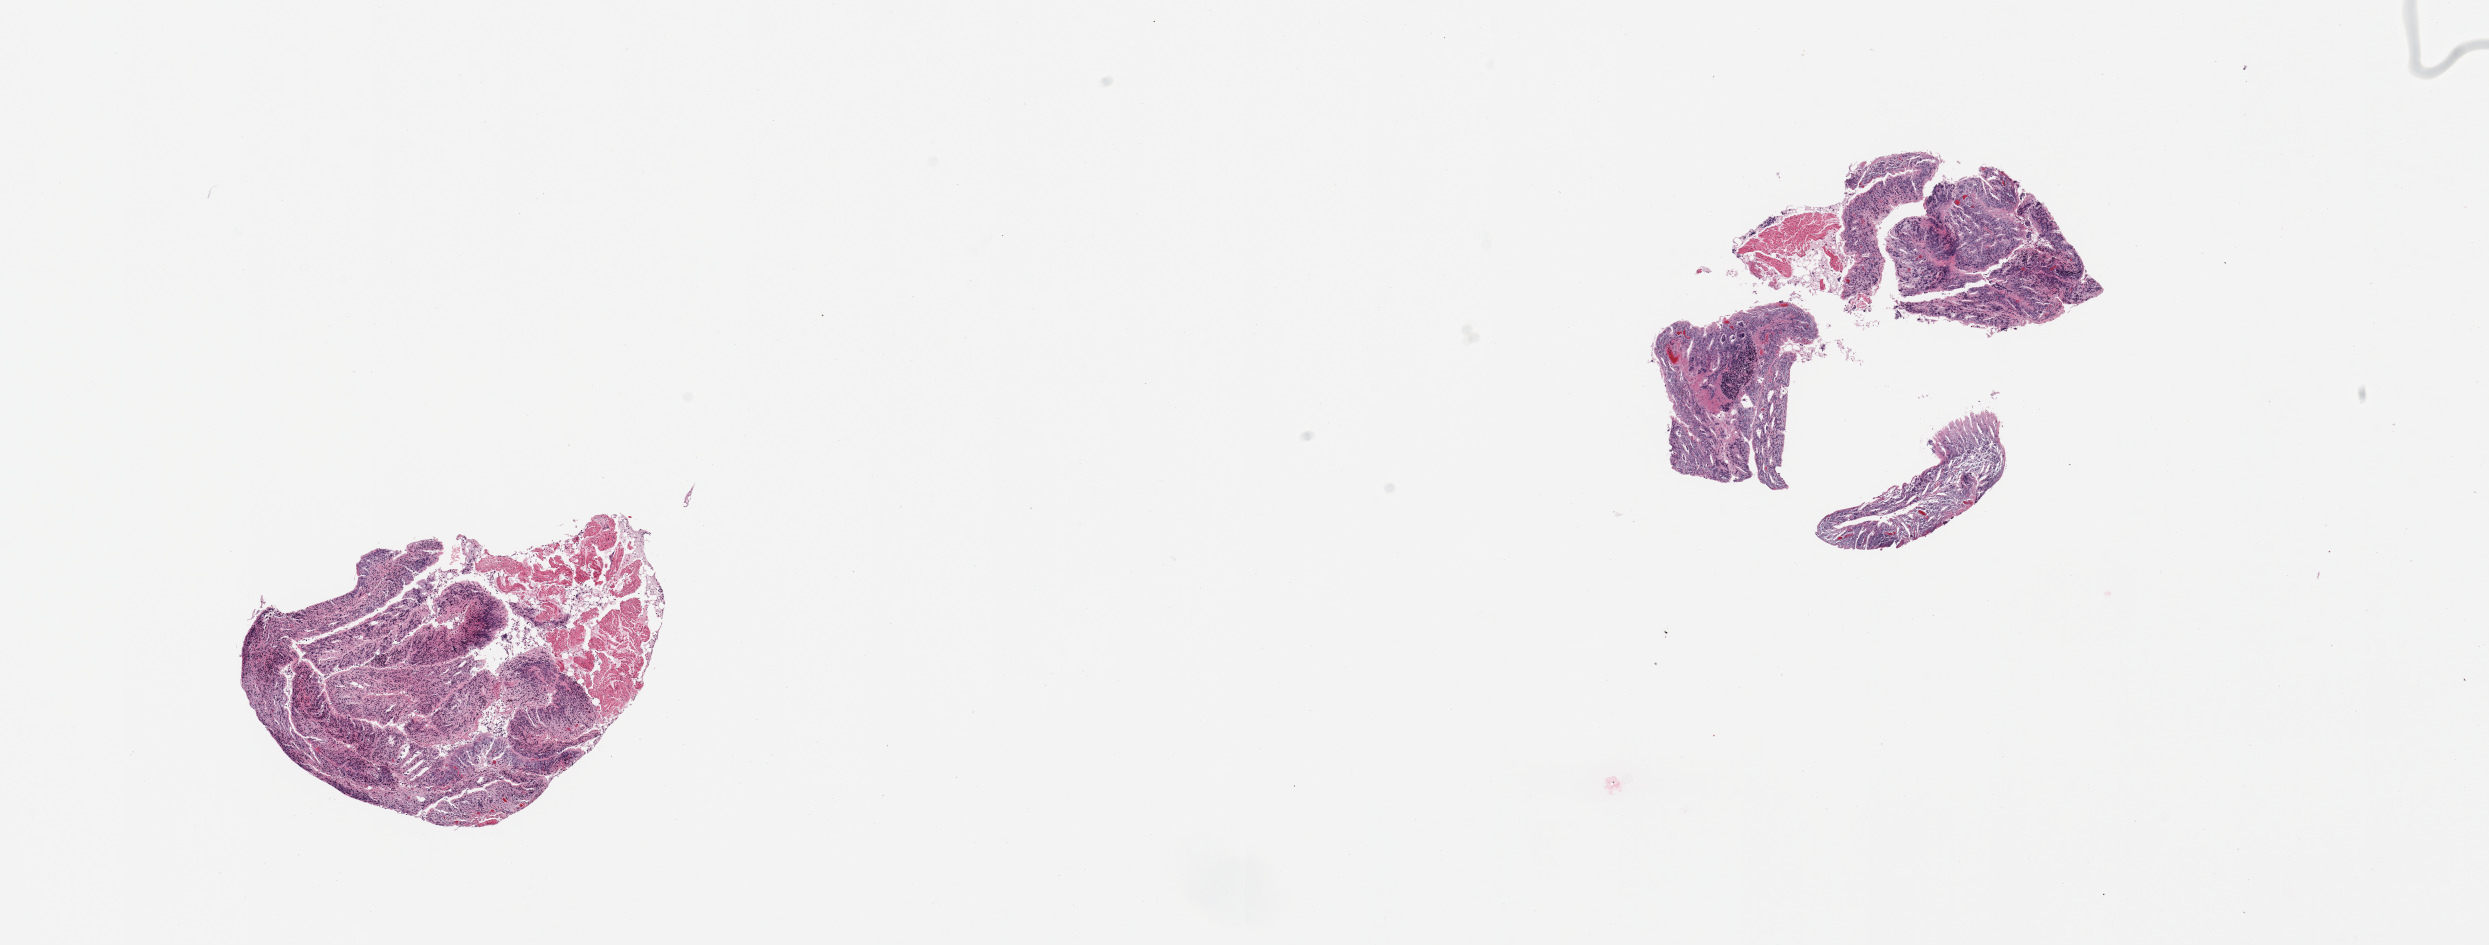
H&E whole-slide image, brightfield — whole scanned area (about 19.7 x 7.5 mm, slide scanned at 20x) shown as a low-resolution overview. PAXgene-fixed, paraffin-embedded tissue. Target tissue: ileum. Donor tissue sample.
* reviewer comment on this tissue sample: 2 fragmented and autolyzed pieces with 1 lymphoid nodule